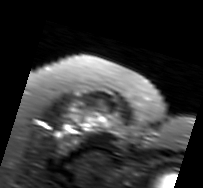
MRI of an extremity soft-tissue mass, one axial slice. Slice 65 of 91 in the series (ordered by position). T2-weighted fat-saturated. MR volume resampled by the dataset authors to the PET/CT grid (not the native acquisition matrix). 3.27 mm slice thickness. 203 × 188 image matrix. Female patient. From the clinical record (not read from this slice): histological type: malignant solitary fibrous tumor; grade: intermediate; site of the primary tumour: right thigh.
Annotated regions visible in this slice (expert contour drawn on MRI and transferred to this co-registered scan by the dataset authors):
- gross tumour volume including surrounding oedema: bounding box [x1, y1, x2, y2] px = [58, 106, 123, 148]